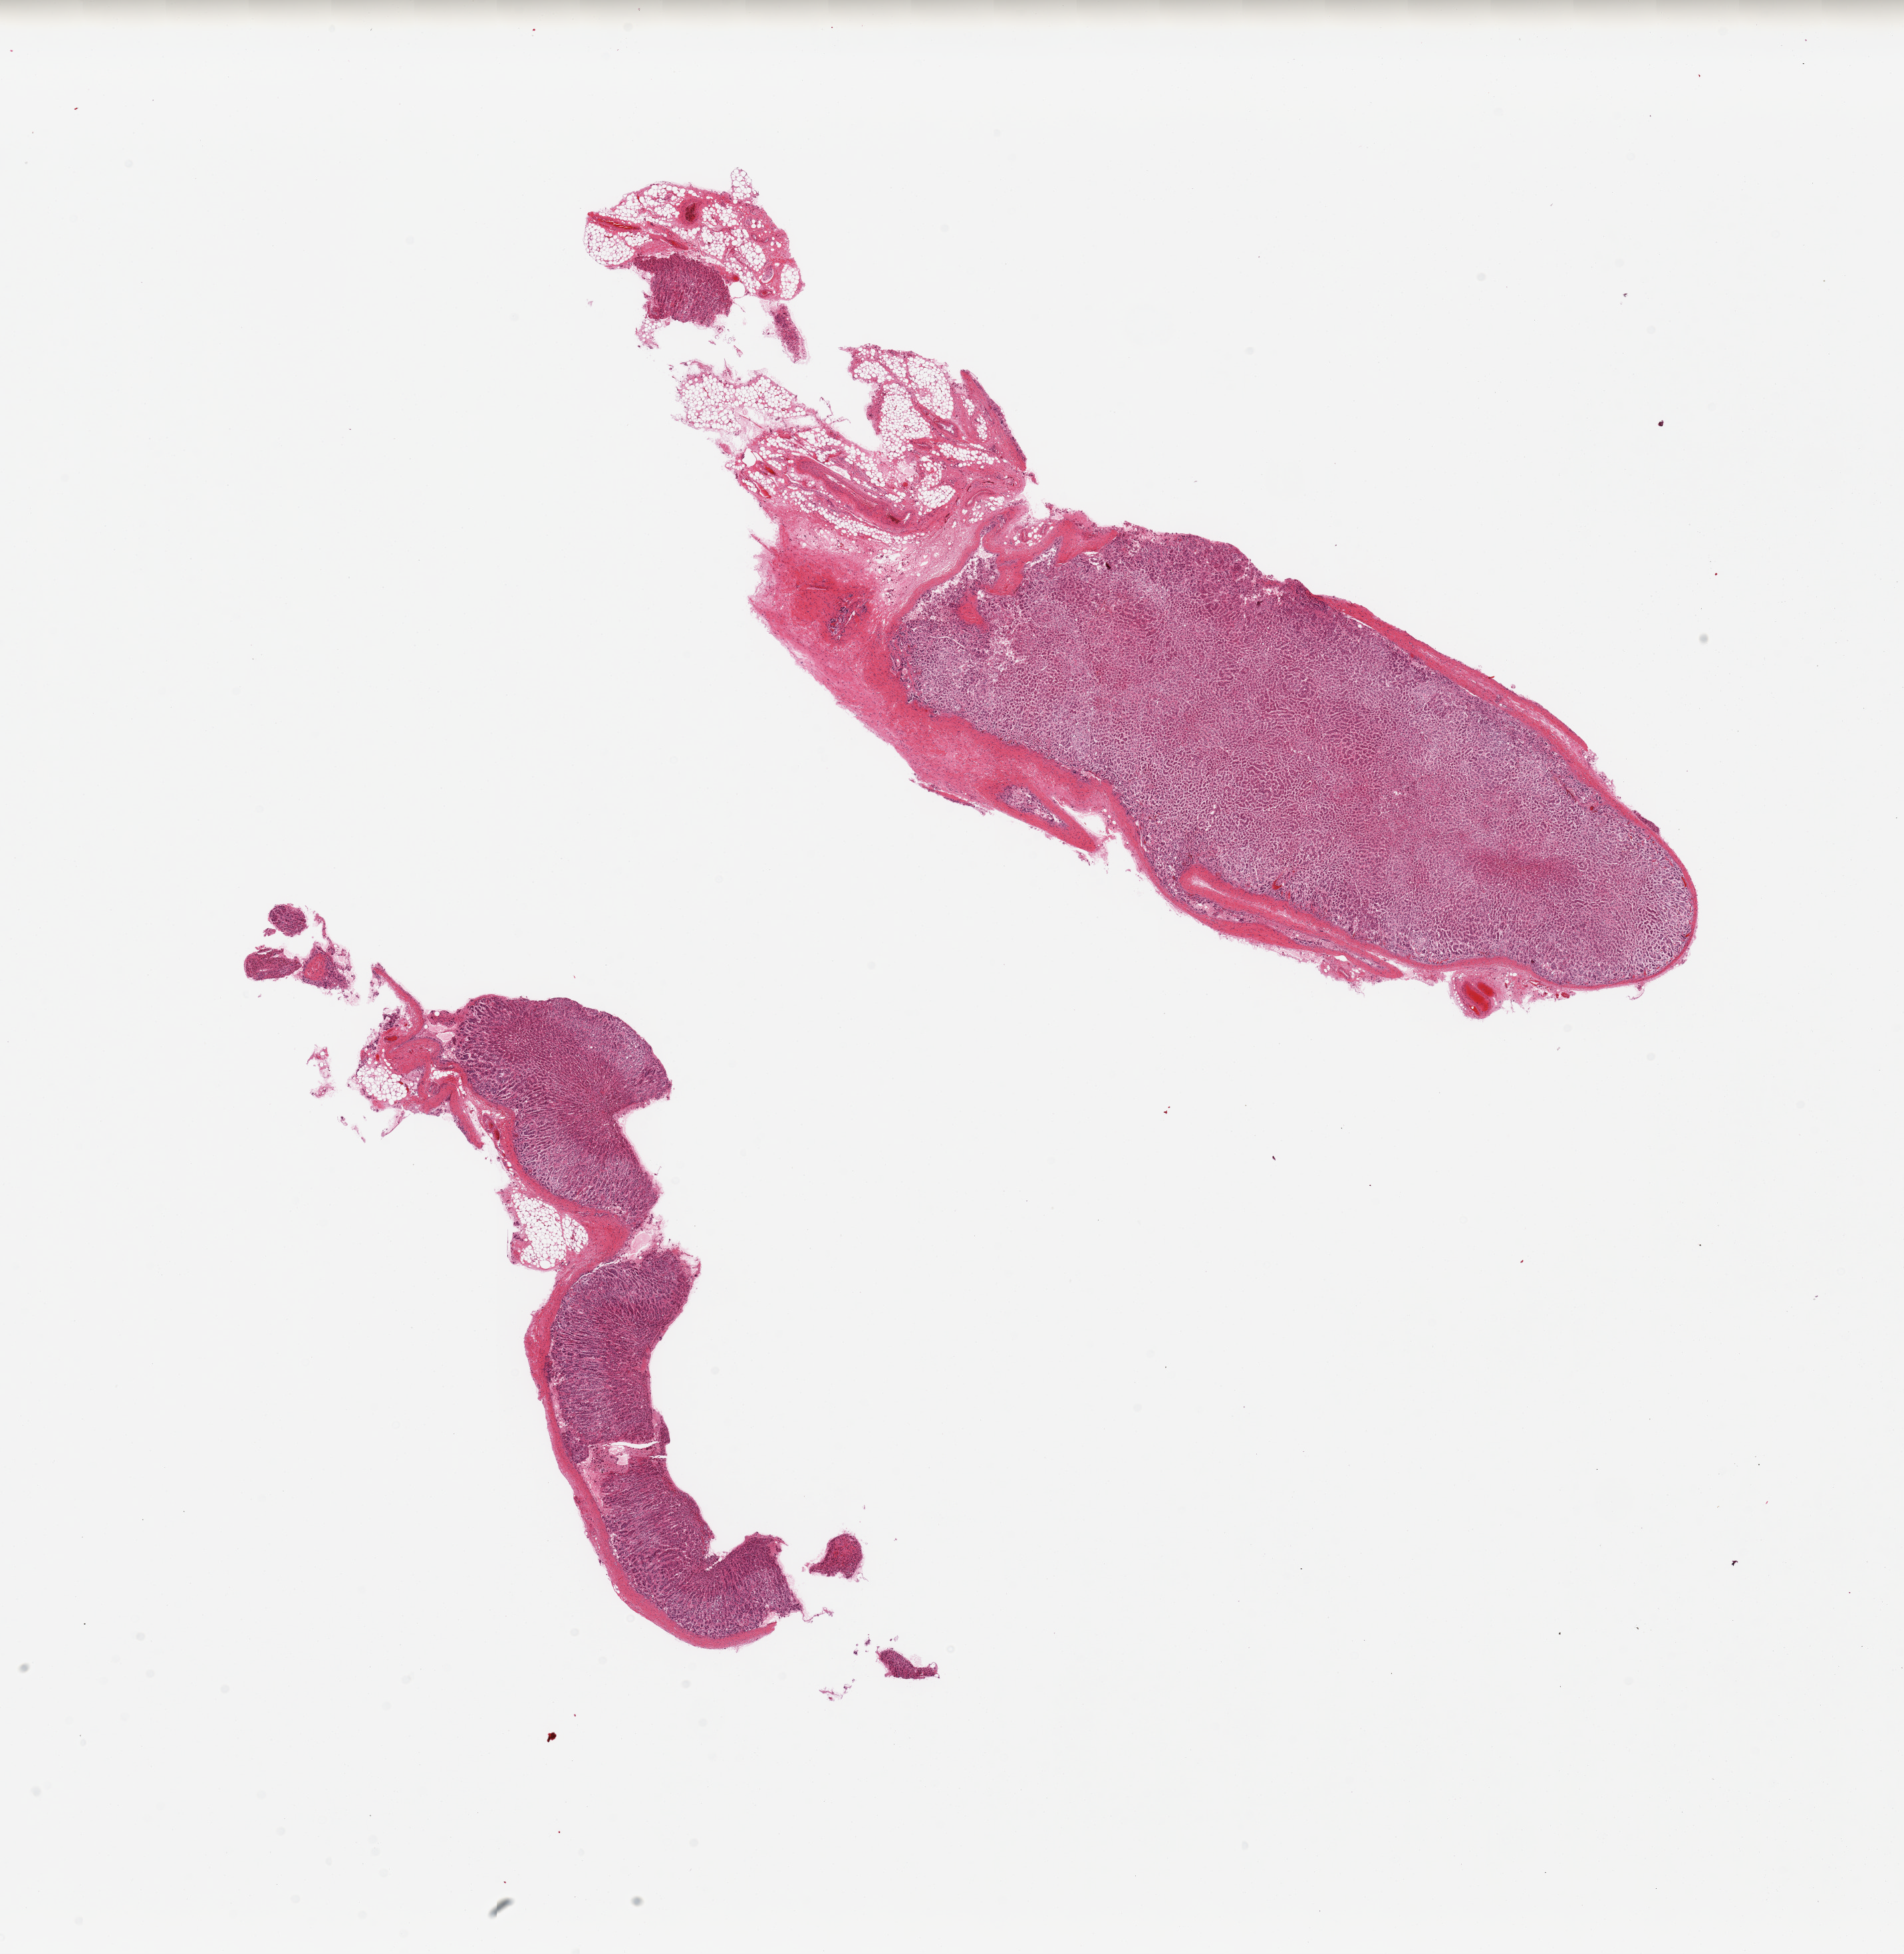
Whole-slide image, H&E stain, shown as a low-resolution overview of the whole scanned area (about 22.6 x 23.2 mm, acquisition: 20x scan), PAXgene-fixed, paraffin-embedded tissue, target tissue: adrenal gland, donor tissue sample. Male donor.
Review note (as recorded): 2 pieces, moderately-severe autolyzed cortex, adherent fat/fibrous tissue is ~30% of specimens.